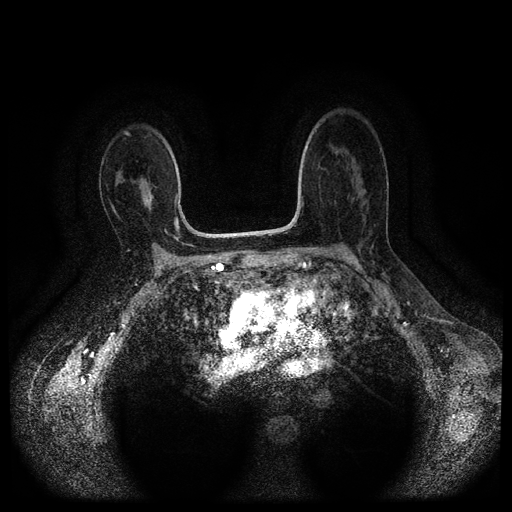
Breast MRI (dynamic contrast-enhanced, multi-phase), one axial slice. Position 59 of 112 along the scan axis. Dynamic contrast-enhanced series, time point 2 of 5 at this slice position (early post-contrast). 1.5 T. TE 2.6 ms, TR 5.4 ms. 2 mm slice thickness. 512 × 512 image matrix. Patient: female, 53 years.
Outlined on this slice (semi-automatic segmentation, software-assisted and operator-edited):
- breast lesion (labelled 'tumour' in the annotation; benign lesions carry a separate 'benign' label): bounding box (x1, y1, x2, y2) in pixels: (136, 179, 154, 212)